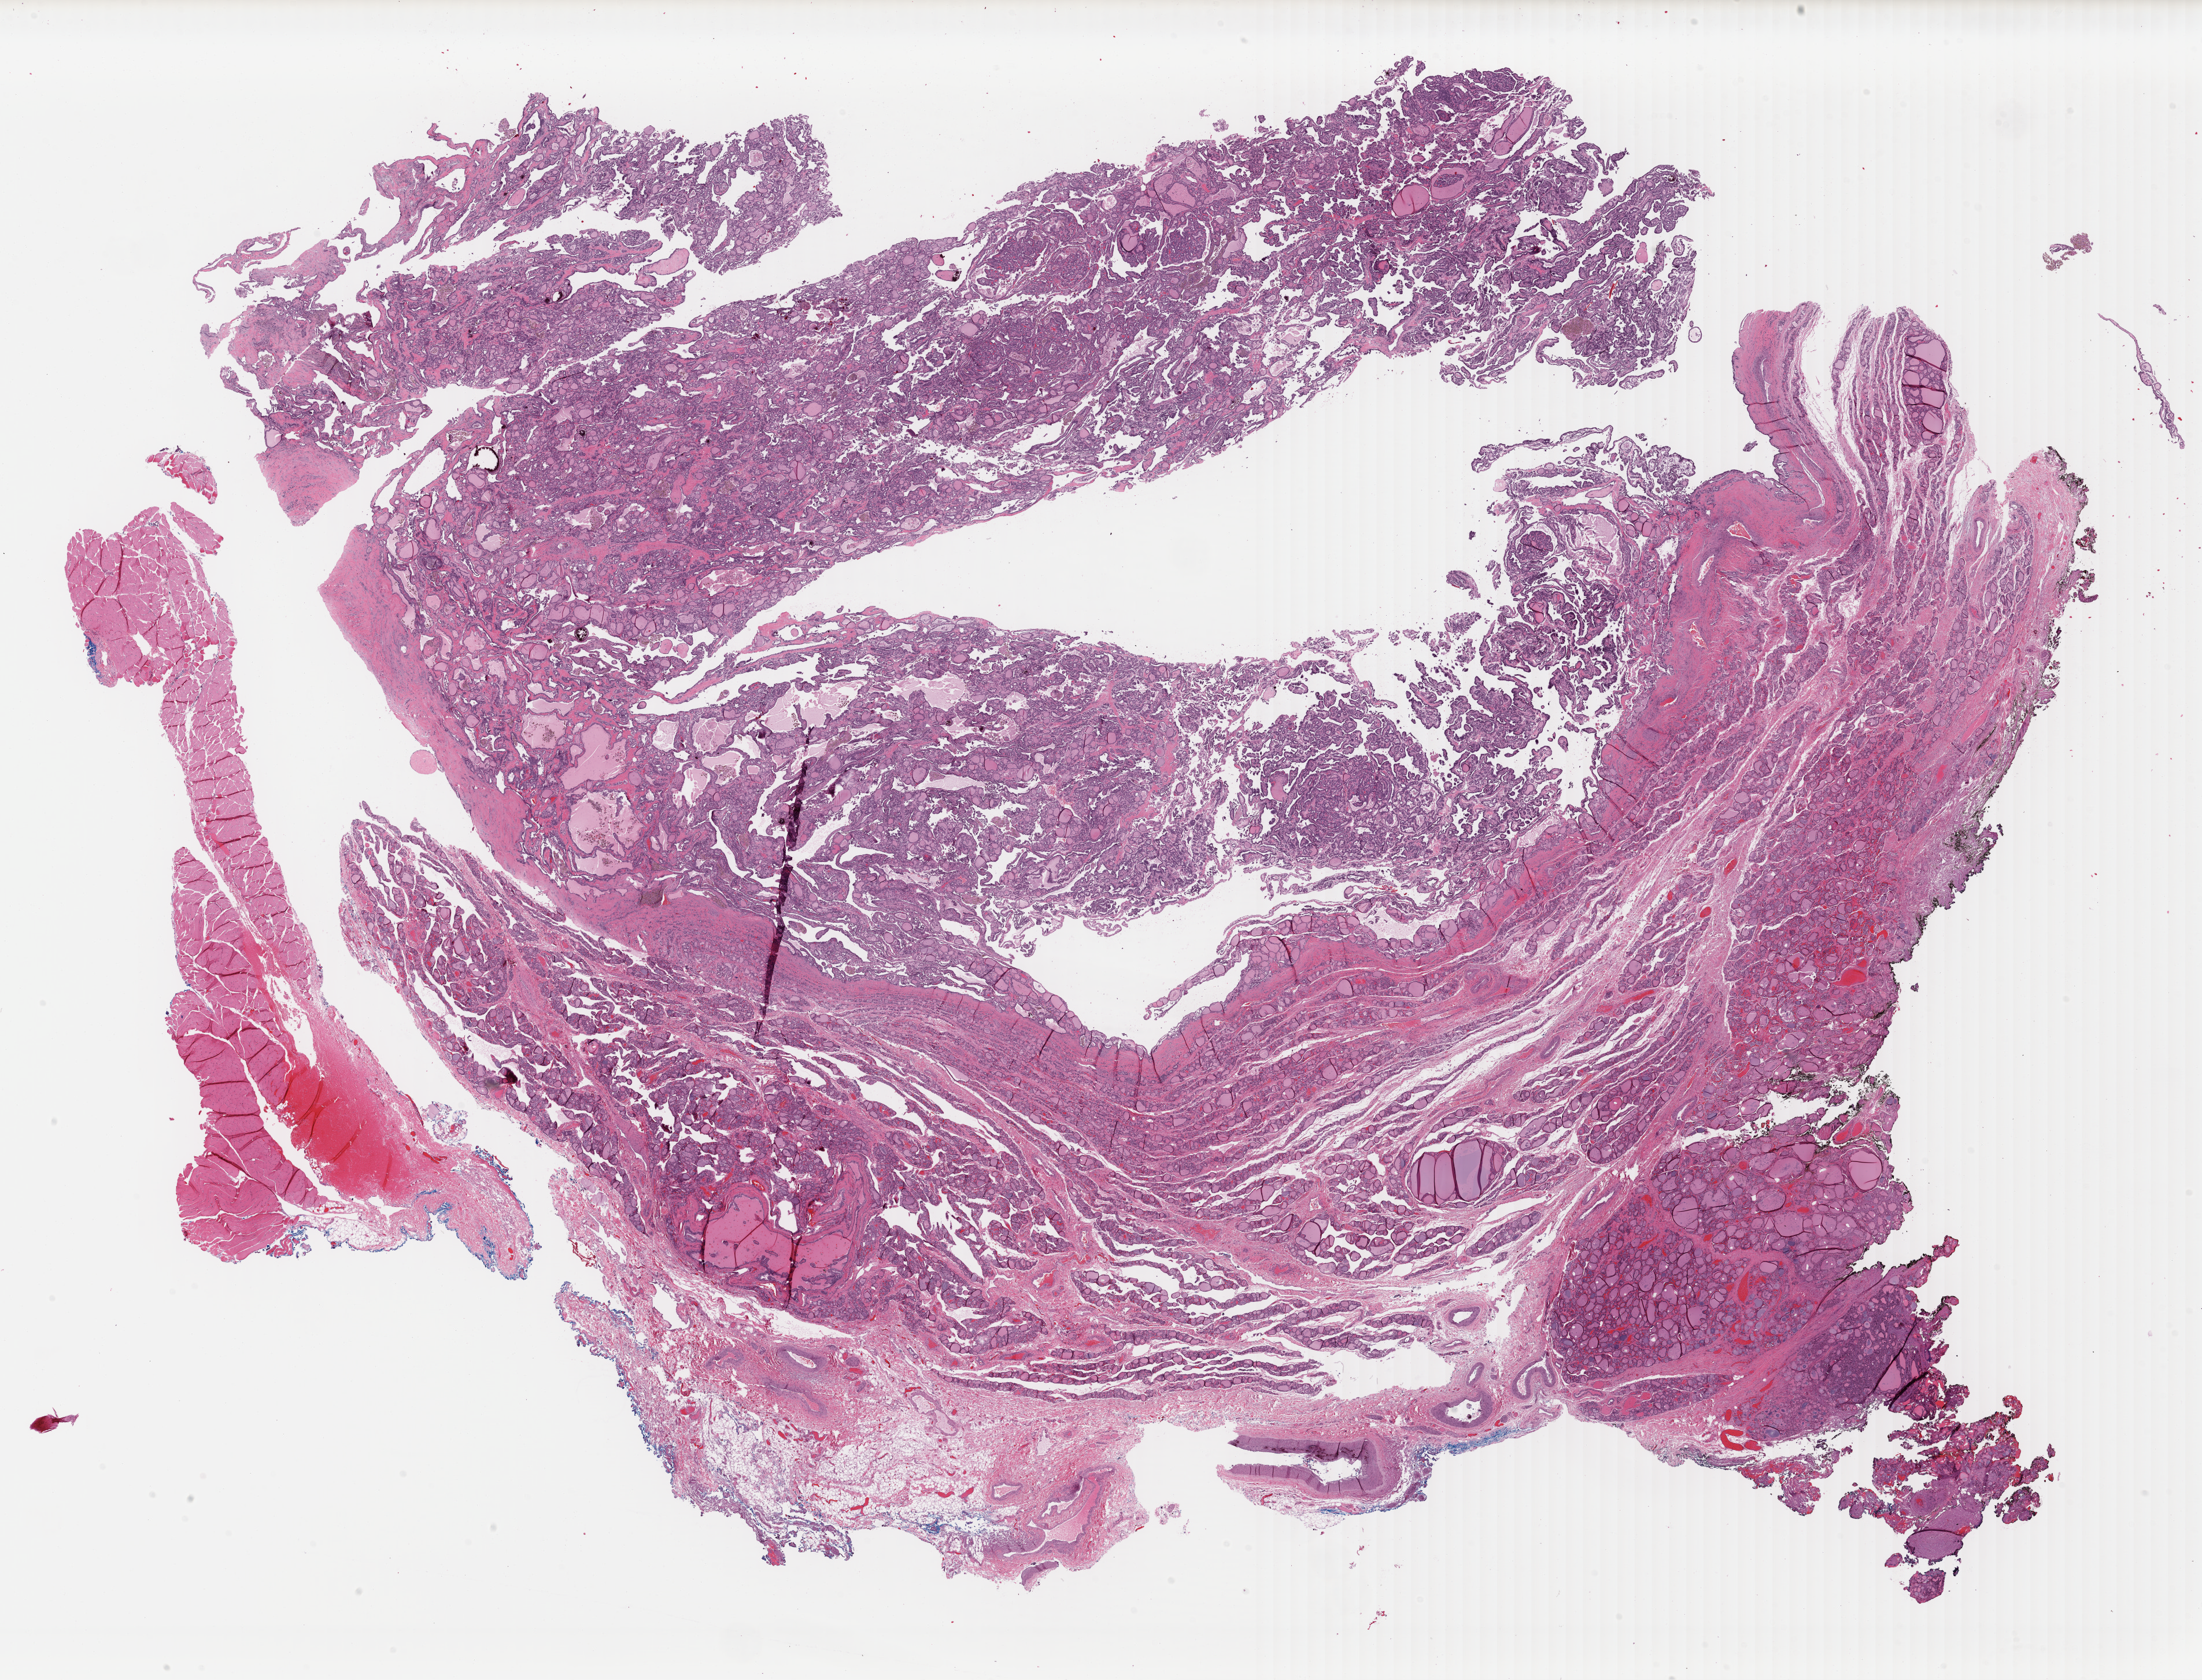
Digitized Hematoxylin and eosin (H&E) stained tissue section (whole slide) — shown as a low-resolution overview of the whole scanned area (about 29.9 x 22.8 mm); formalin-fixed paraffin-embedded (FFPE) diagnostic section; thyroid, primary tumour sample. Female, age 52 years at initial diagnosis.
* AJCC pathologic stage: II (7th edition)
* diagnosis: Papillary adenocarcinoma, NOS (thyroid gland)